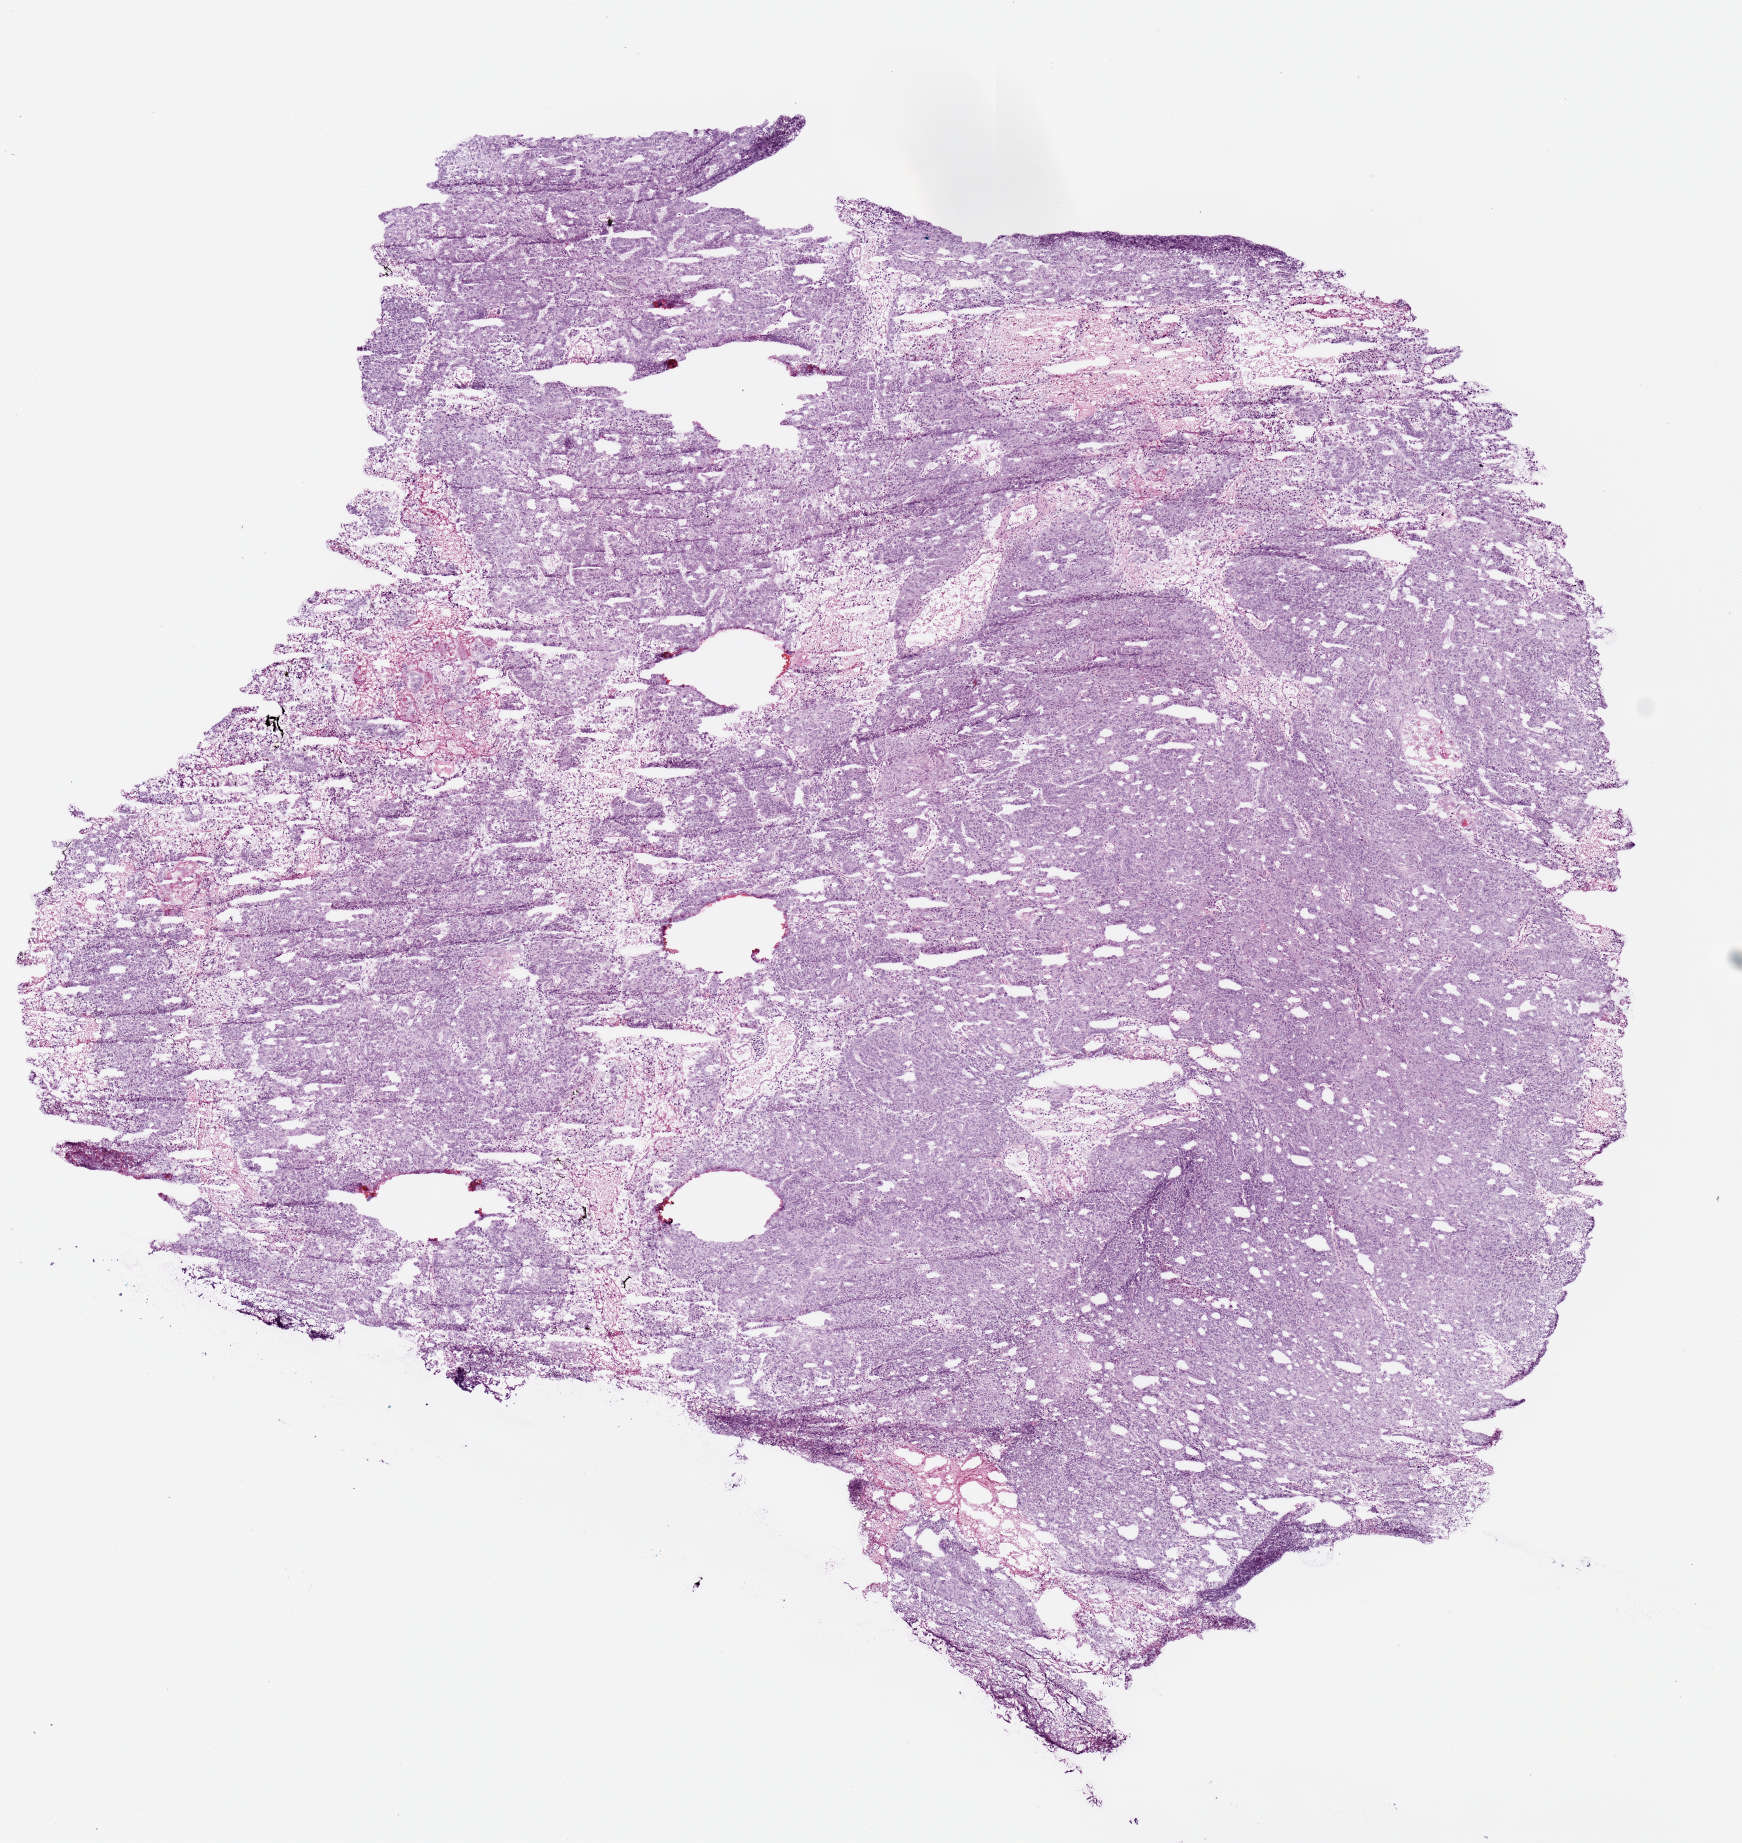
H&E-stained whole-slide image — whole scanned area (about 6.9 x 7.3 mm) shown as a low-resolution overview. Frozen section. Sample: primary tumour, uterus. Patient: female, age at initial diagnosis 58 years. Histologic grade: G3 (poorly differentiated). Slide review estimates, as recorded: tumour cells 97%, tumour nuclei 80%, normal cells 0%, stromal cells 0%, necrosis 3%. Inflammatory infiltration, as recorded: lymphocyte infiltration 0%, monocyte infiltration 0%, neutrophil infiltration 0%.
FIGO stage: IB. Histologic diagnosis: Endometrioid adenocarcinoma, NOS (endometrium).